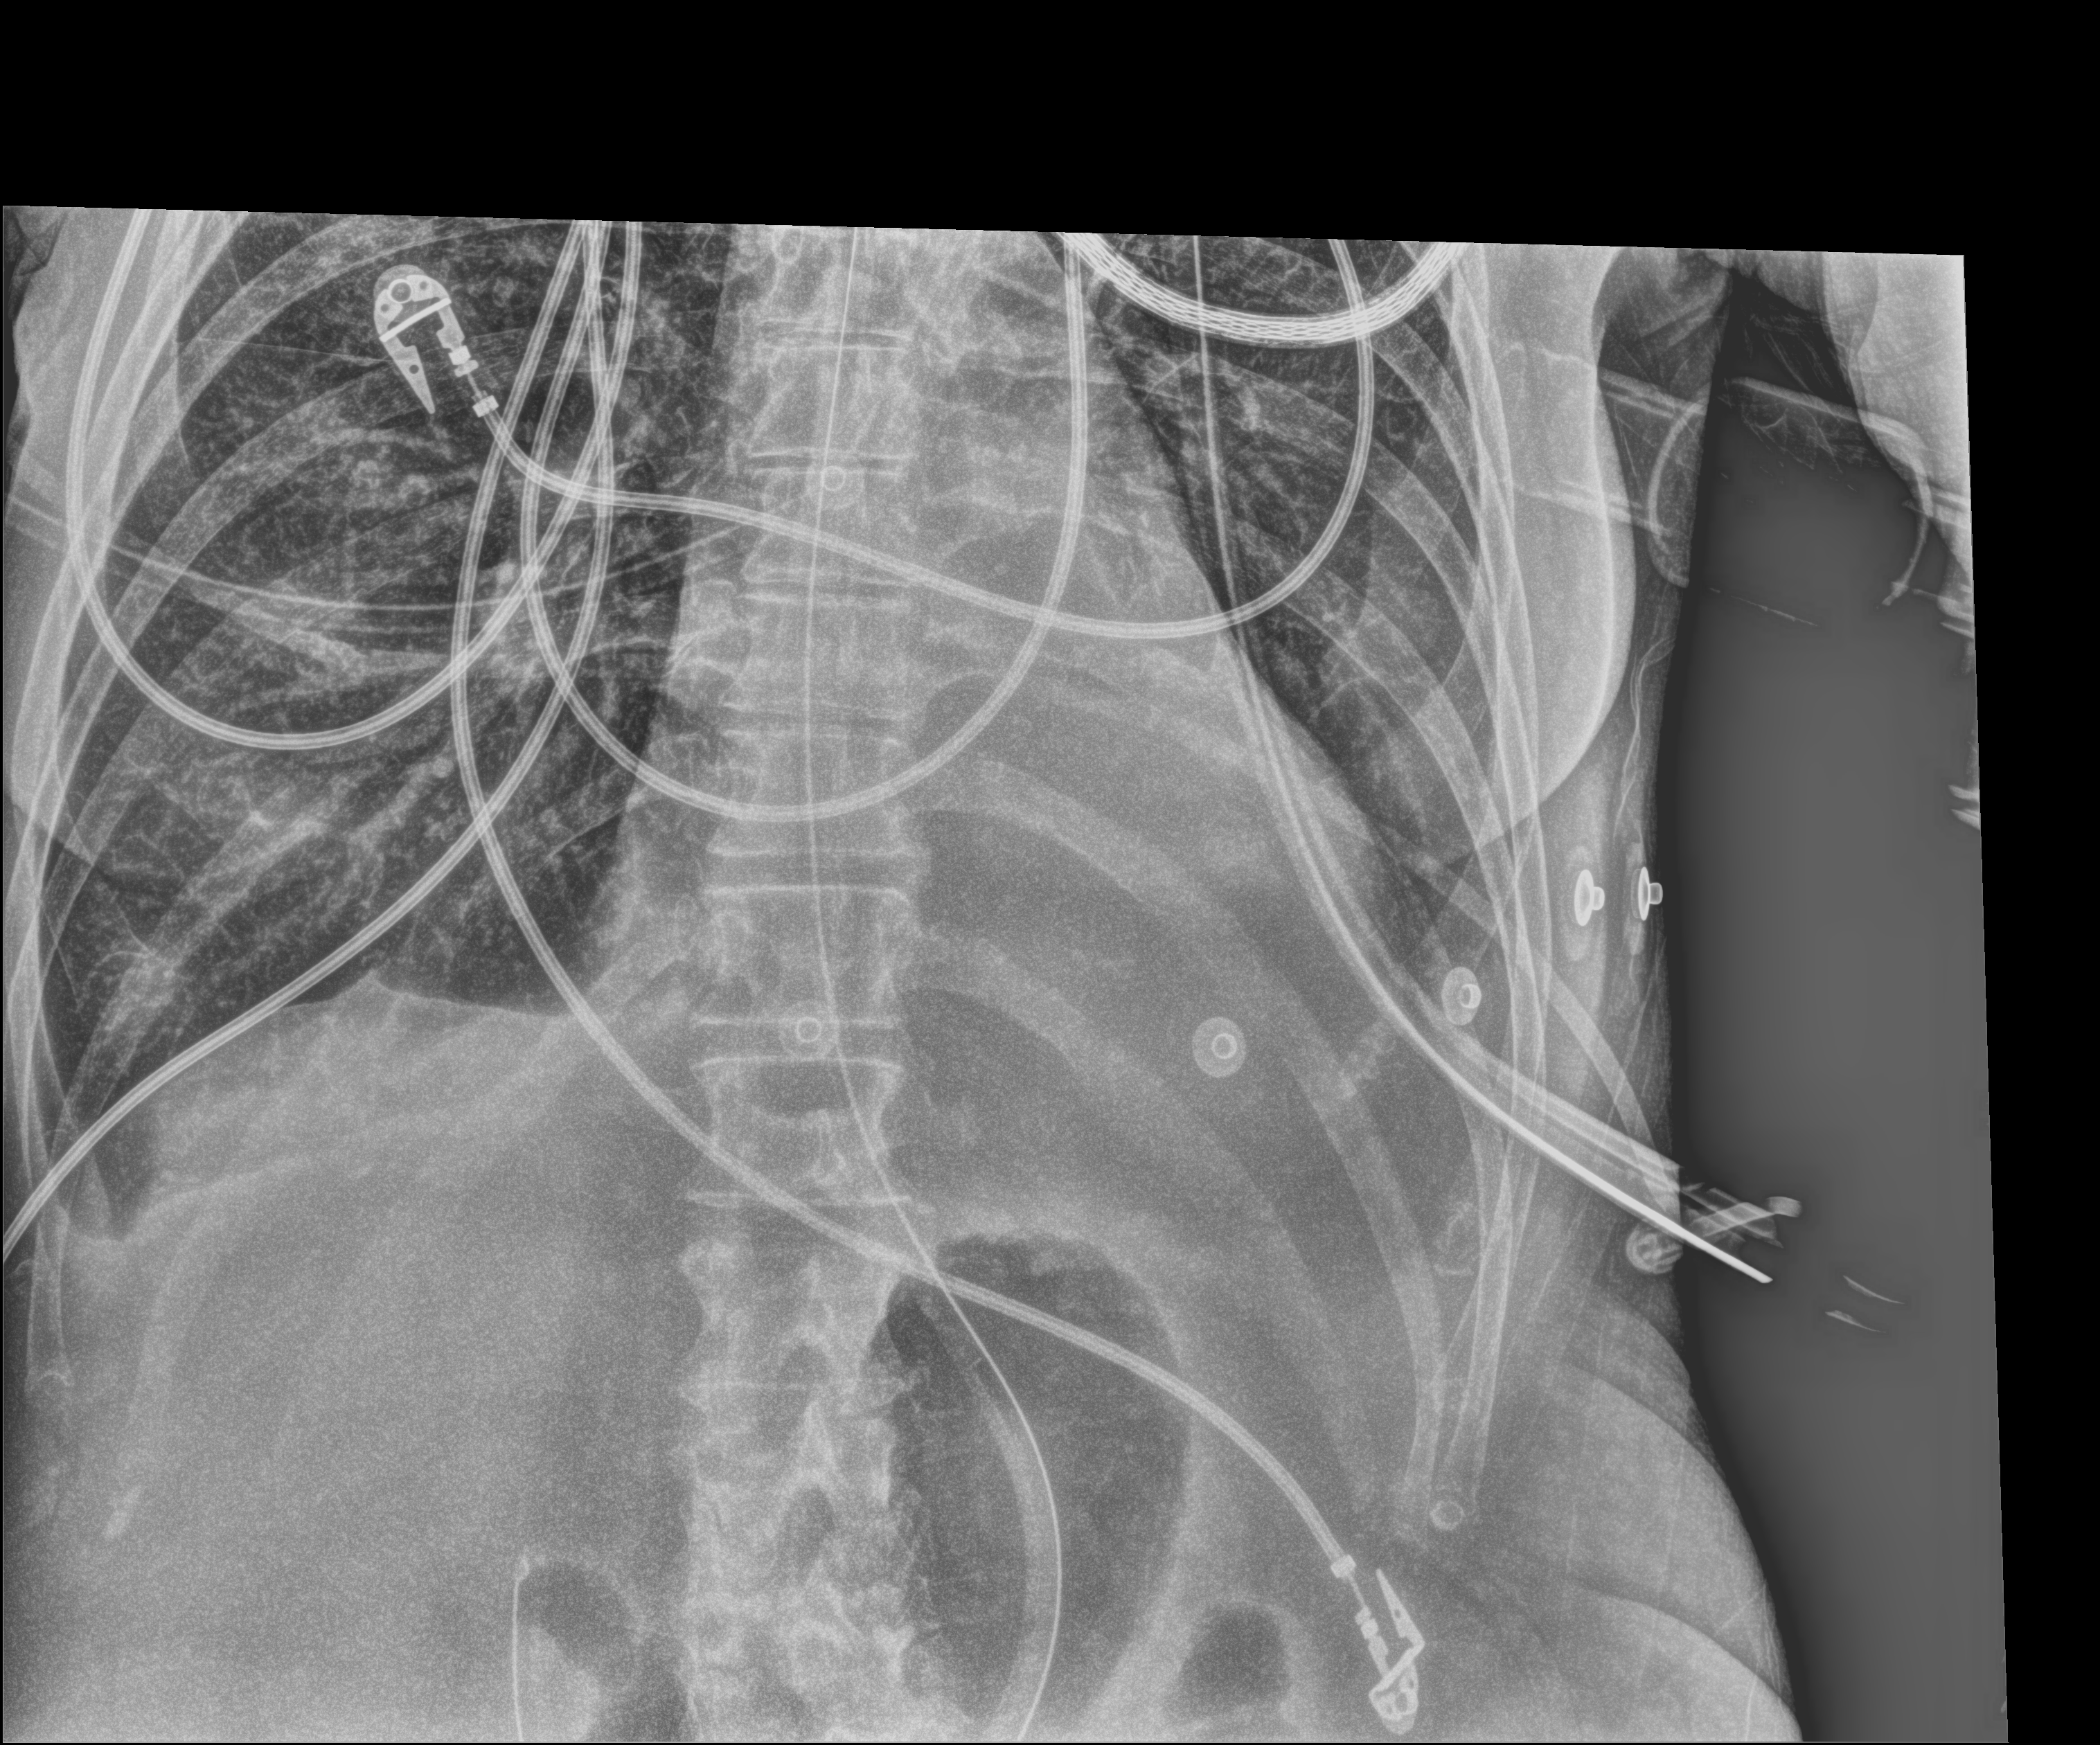
Portable chest radiograph, anteroposterior (AP) projection. Female patient hospitalised with COVID-19, age 60–74 years.
Hospital-stay facts (about this admission, not read from this image; timing relative to this image not recorded): admitted to intensive care during this hospital stay: yes.